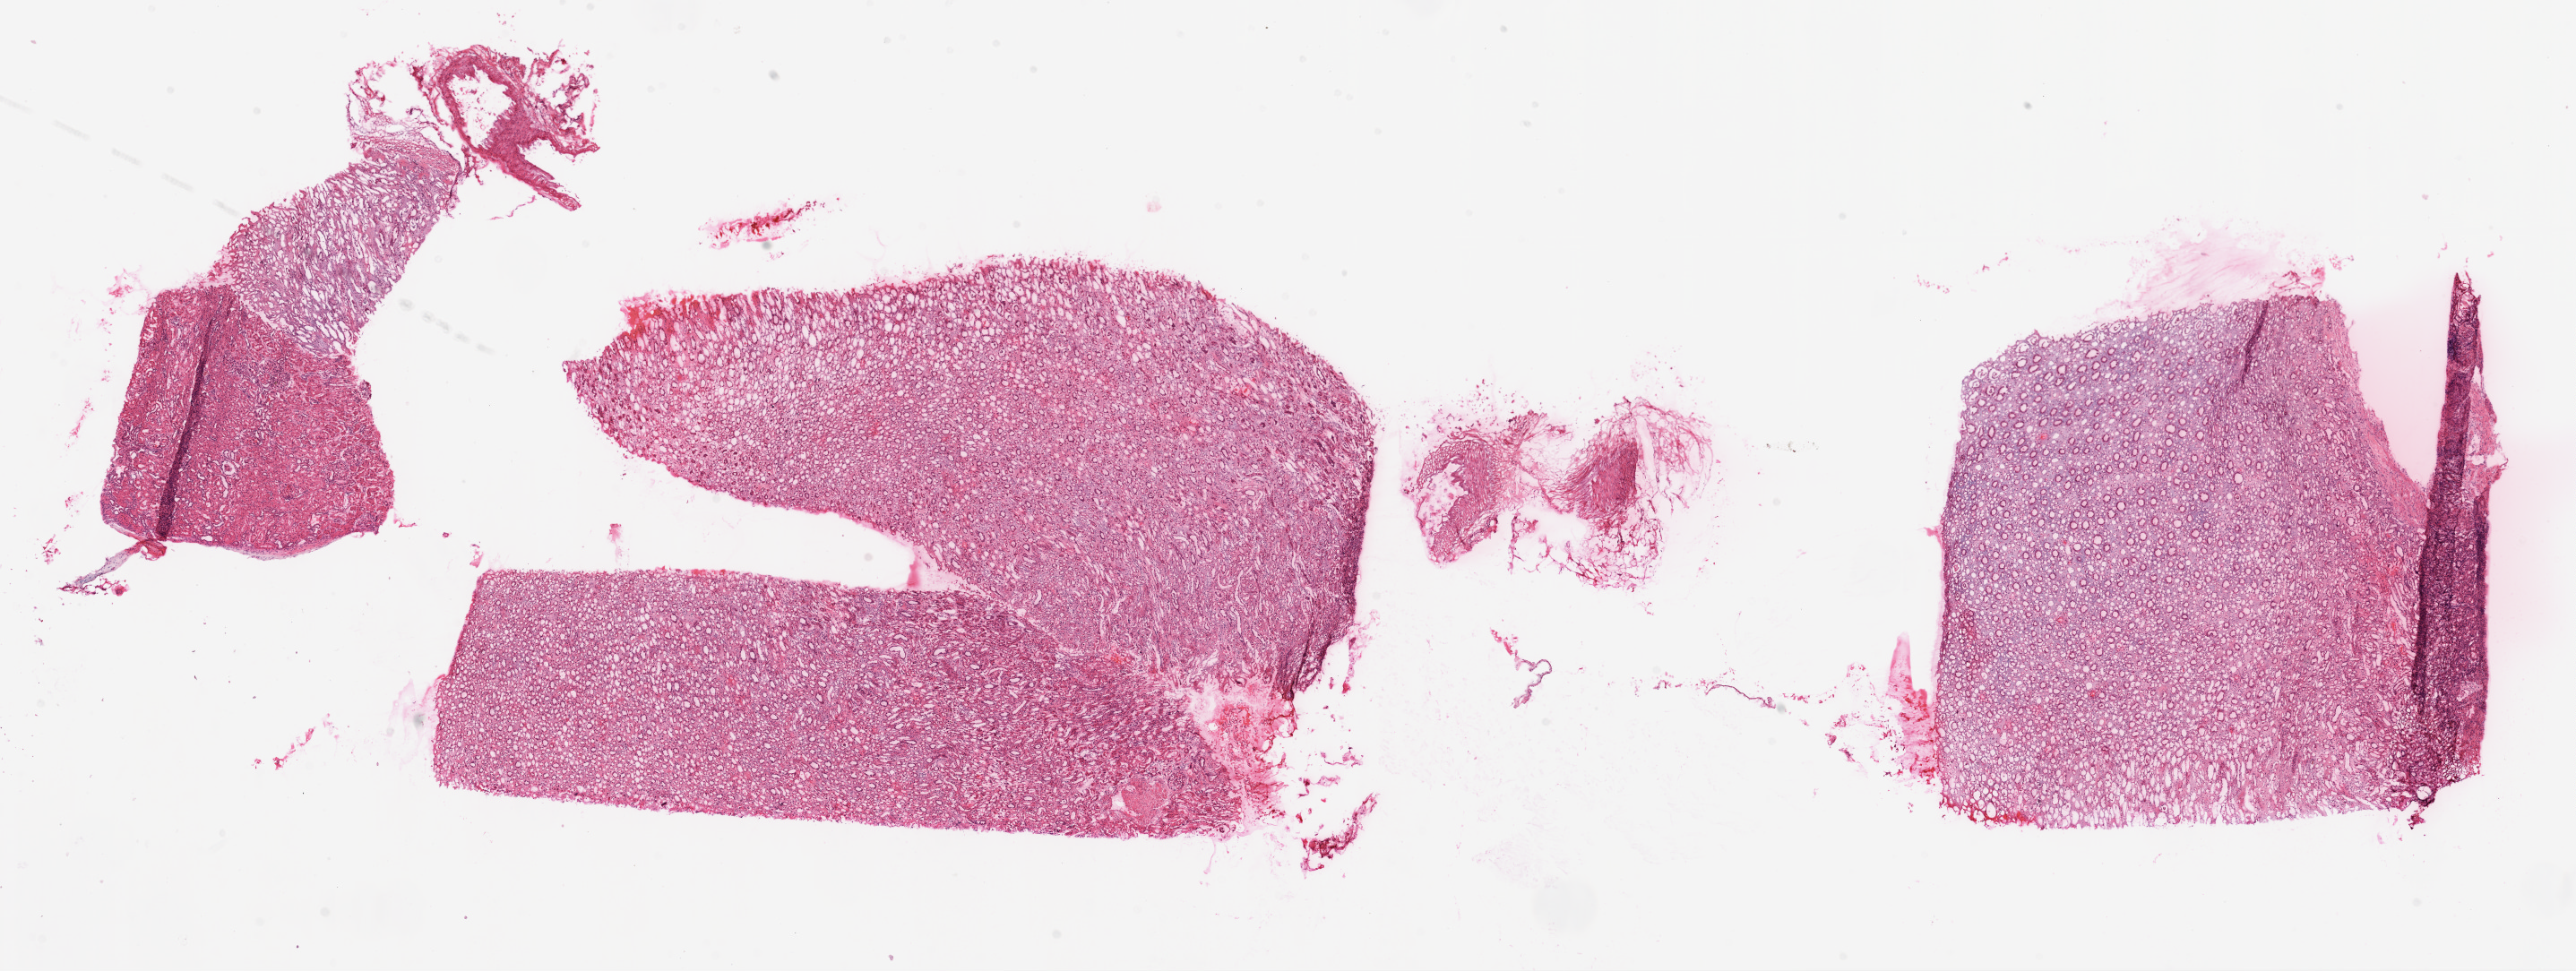
Whole-slide histology image, H&E-stained — shown as a low-resolution overview of the whole scanned area (about 23.1 x 8.7 mm, slide scanned at 20x), frozen section from the top of the tissue portion, sample: solid tissue normal (non-tumour tissue), kidney. Patient: male, age at initial diagnosis 61 years.
This section: solid tissue normal (non-tumour) sample from the same patient. Patient diagnosis: Clear cell adenocarcinoma, NOS.